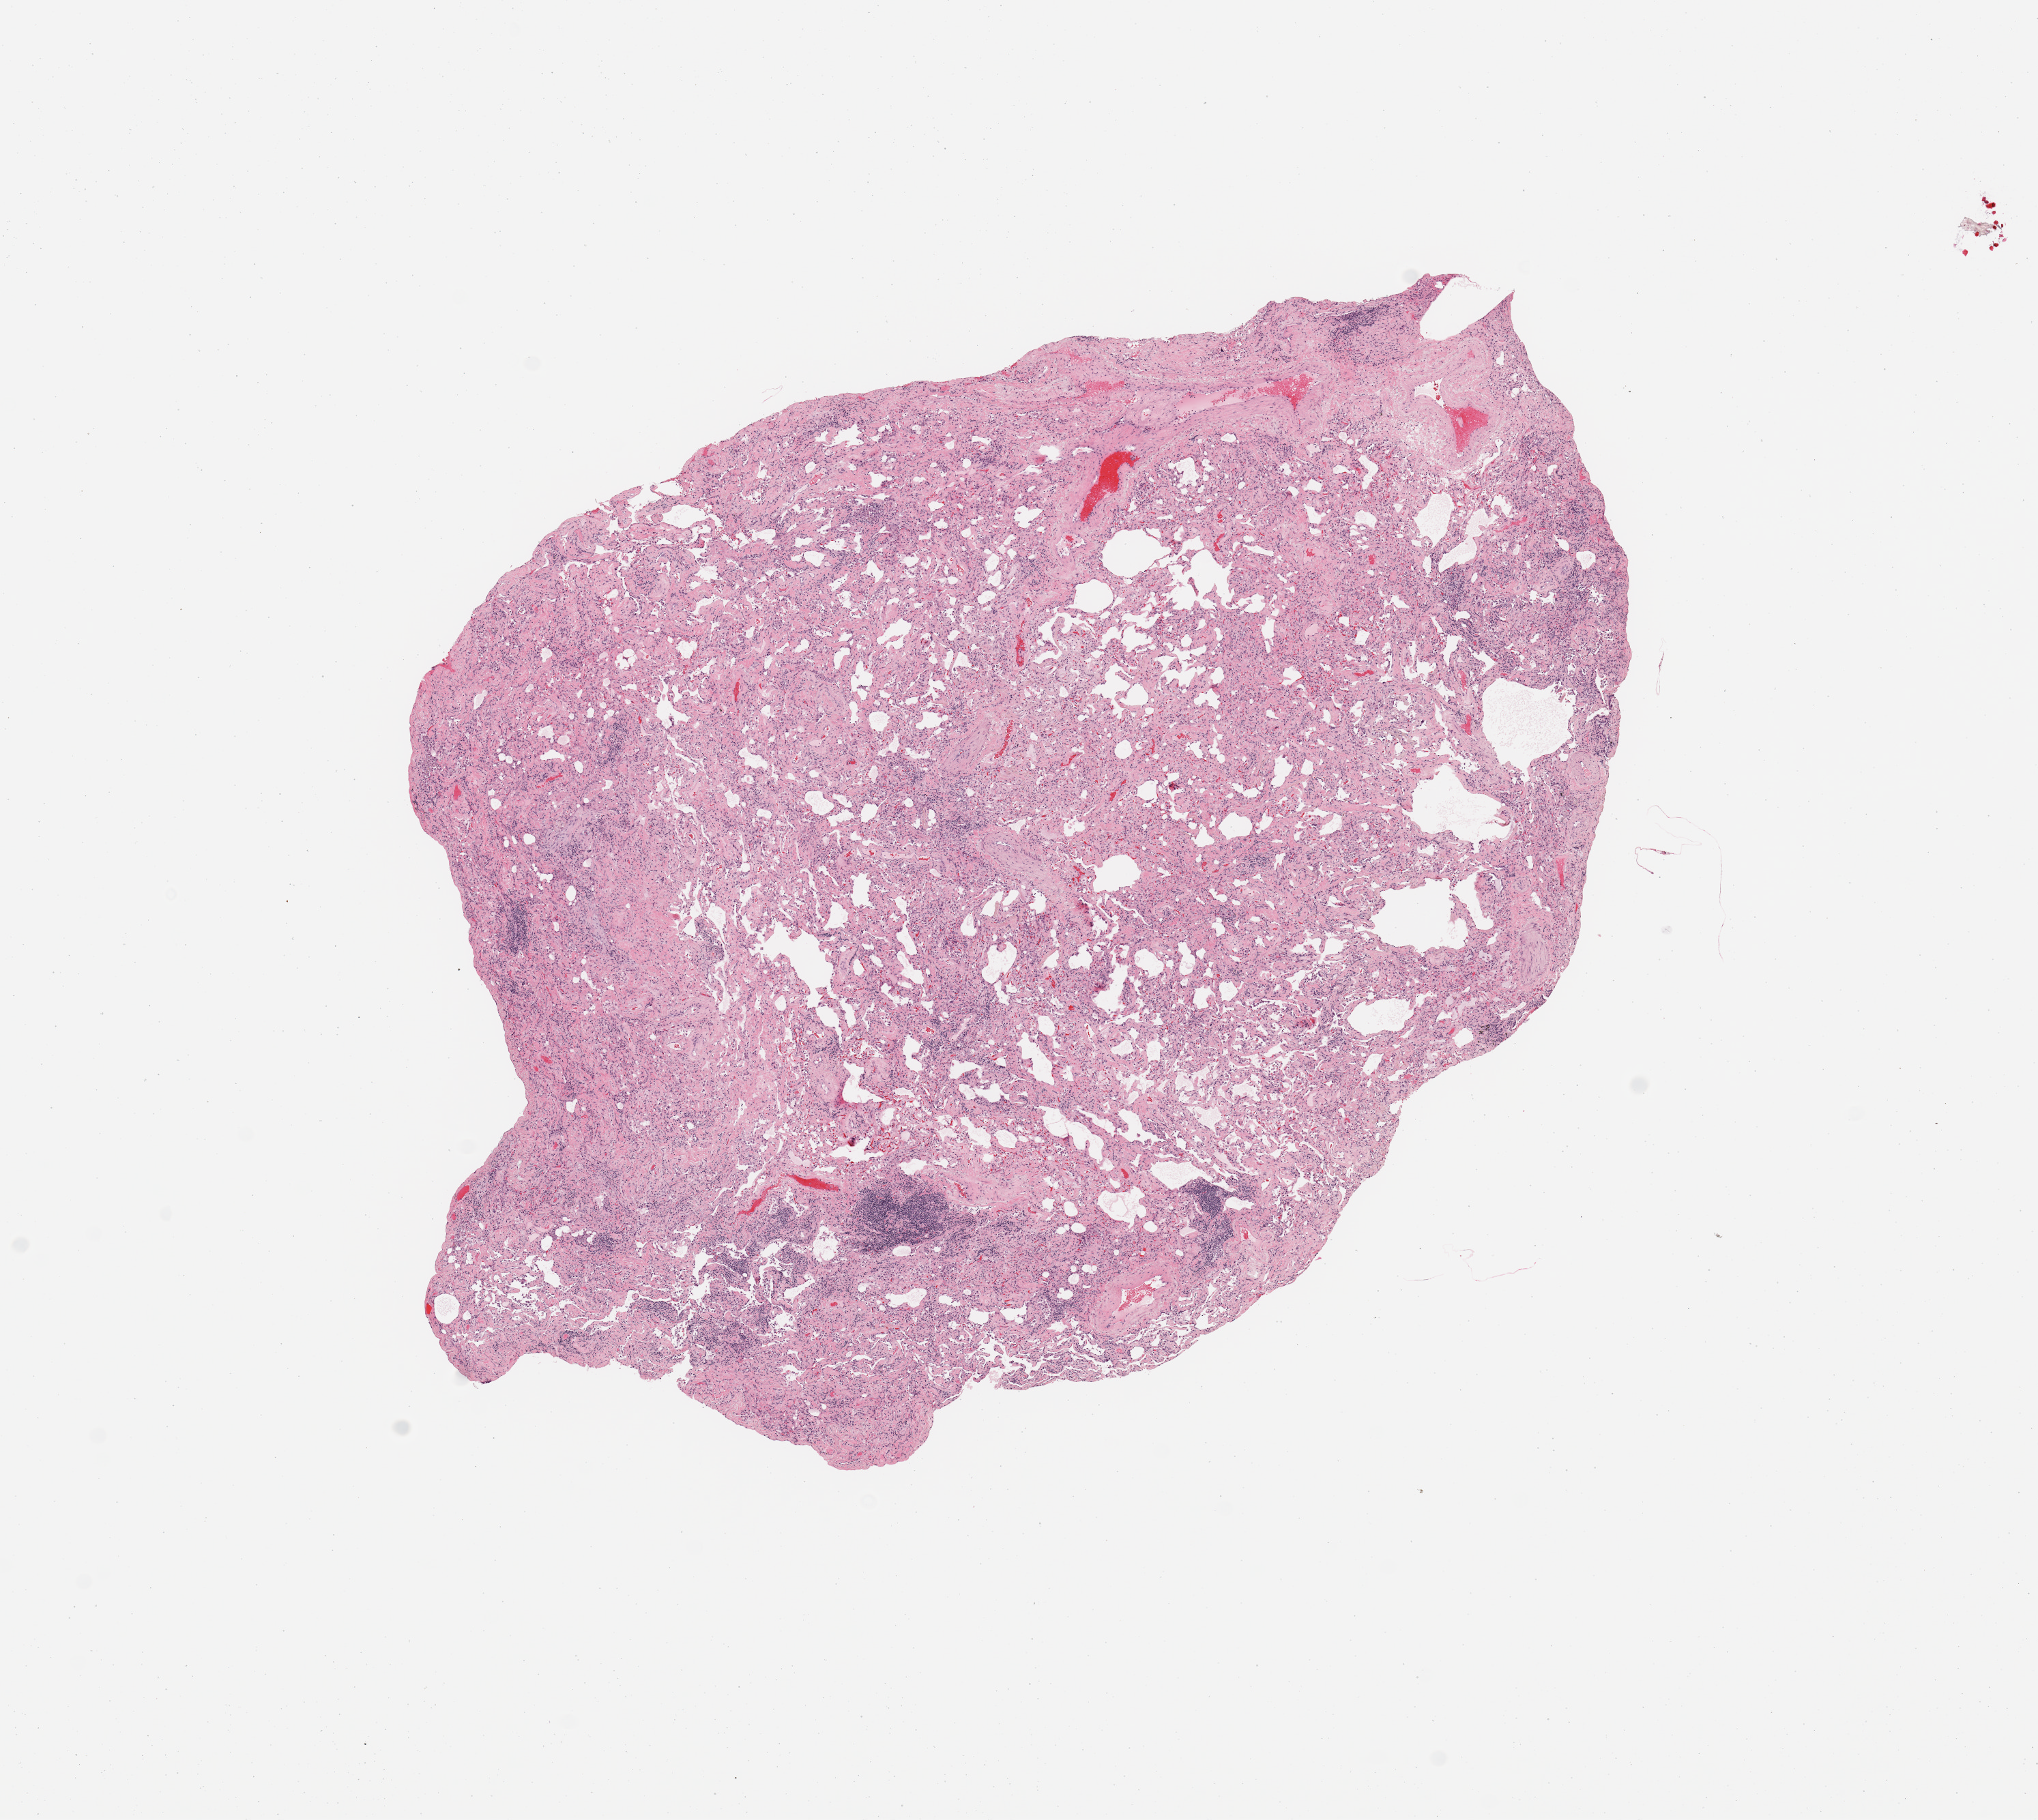
H&E-stained whole-slide image — whole scanned area (about 11.8 x 10.6 mm, slide scanned at 20x) shown as a low-resolution overview, normal (non-tumour) tissue sample, sampled site: lung. Female, 74 y/o.
This section: normal (non-tumour) tissue from the same patient. Patient diagnosis: Squamous cell carcinoma, NOS.